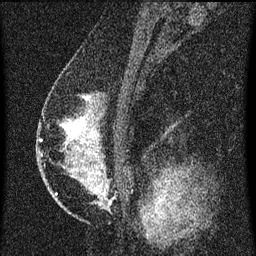
Breast MRI (dynamic contrast-enhanced), one sagittal slice. Slice 37 of 60 in the series (ordered by position). Dynamic contrast-enhanced series, image 2 of 3 at this slice position (ordered by acquisition). 1.5 T. TE 4.2 ms, TR 8 ms. 2 mm slice thickness. 256 × 256 image matrix. Female patient, age 47 years.
Annotated regions visible in this slice (semi-automatically segmented with operator editing):
- analysis volume of interest (the breast-tissue region the enhancement analysis was run in; not a lesion): bounding box <50,80,124,203> (left, top, right, bottom; pixels)
- tumour enhancement mask (voxels above the 70 % enhancement threshold inside the analysis volume of interest): <64,98,88,139>